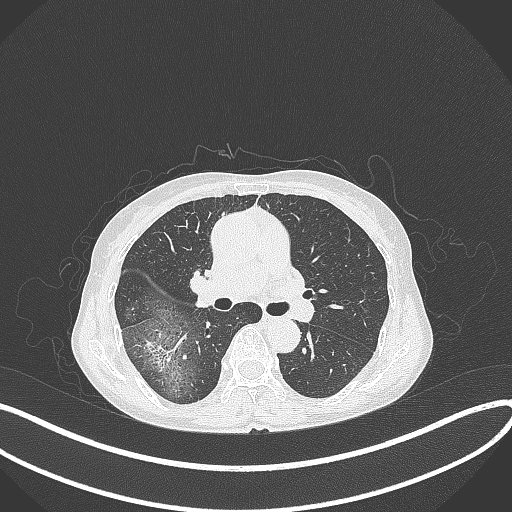
Chest CT, one axial slice. Position 233 of 371 along the scan axis. Reconstruction kernel B70f. 120 kVp. Lung window (W 1500 / L -600 HU). 1 mm slice thickness. 512 × 512 image matrix. Patient: female, 69 years. From the clinical record (not read from this slice): clinical TNM (as recorded): T1b N0 M0.
Outlined on this slice (rectangle marked by the reading radiologist):
- lung tumour (recorded histology: adenocarcinoma): box from (x=138, y=334) to (x=179, y=374) px